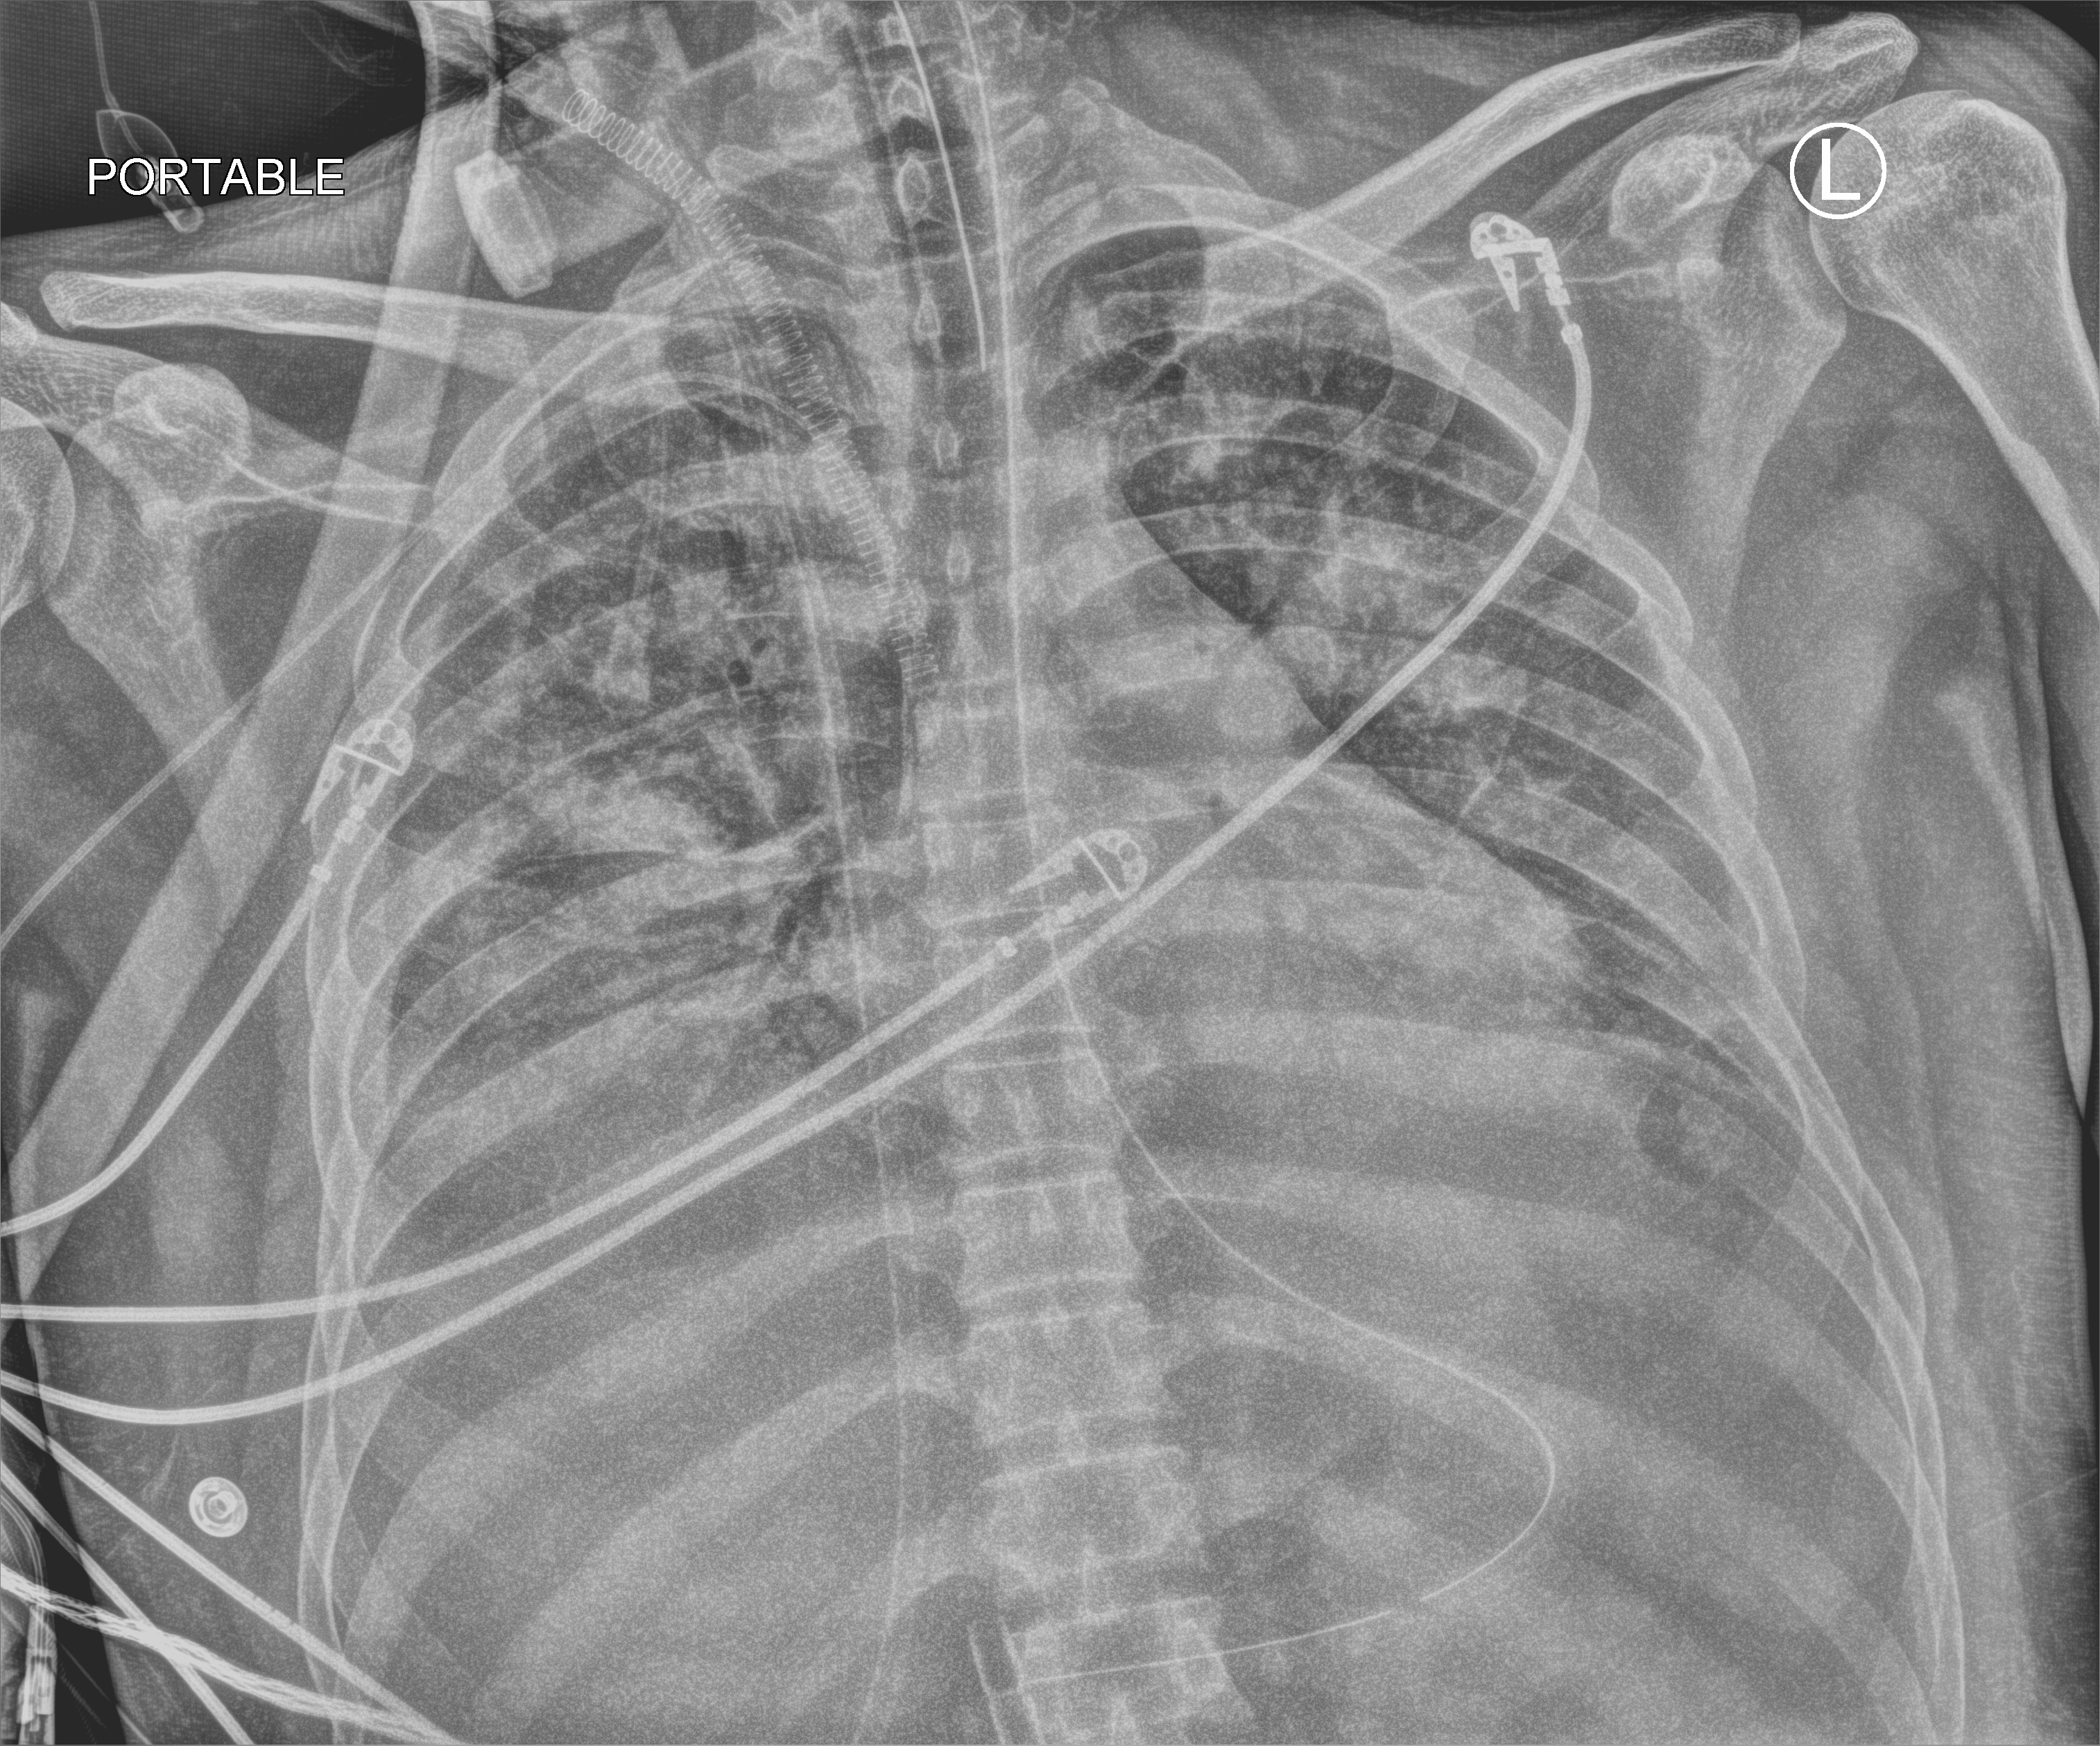
Chest X-ray (portable). Patient hospitalised with COVID-19, aged 18–59 years.
Admission-level facts for this patient (not findings on this image; timing relative to this image not recorded):
- length of hospital stay: 60 days
- admitted to intensive care during this hospital stay: yes